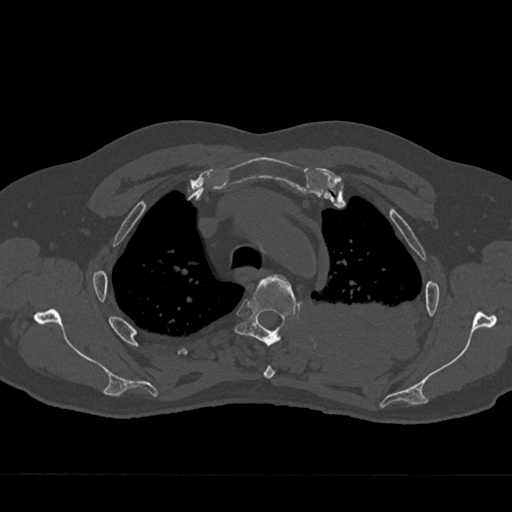
CT including the spine, one axial slice; slice 531 of 797 in the series (ordered by position); reconstruction kernel Br40s/3; 120 kVp; bone window (W 1800 / L 400 HU); 512 × 512 image matrix. Male patient, age 75 years. Case-level facts recorded for this patient, not image findings: primary cancer: renal; vertebrae with lytic lesions (as recorded): T4.
Structures marked on this image (semi-automatic segmentation, software-assisted and operator-edited):
- T3 vertebra: bounding box (x1, y1, x2, y2) in pixels: (263, 365, 275, 379)
- T4 vertebra: (234, 274, 296, 346)